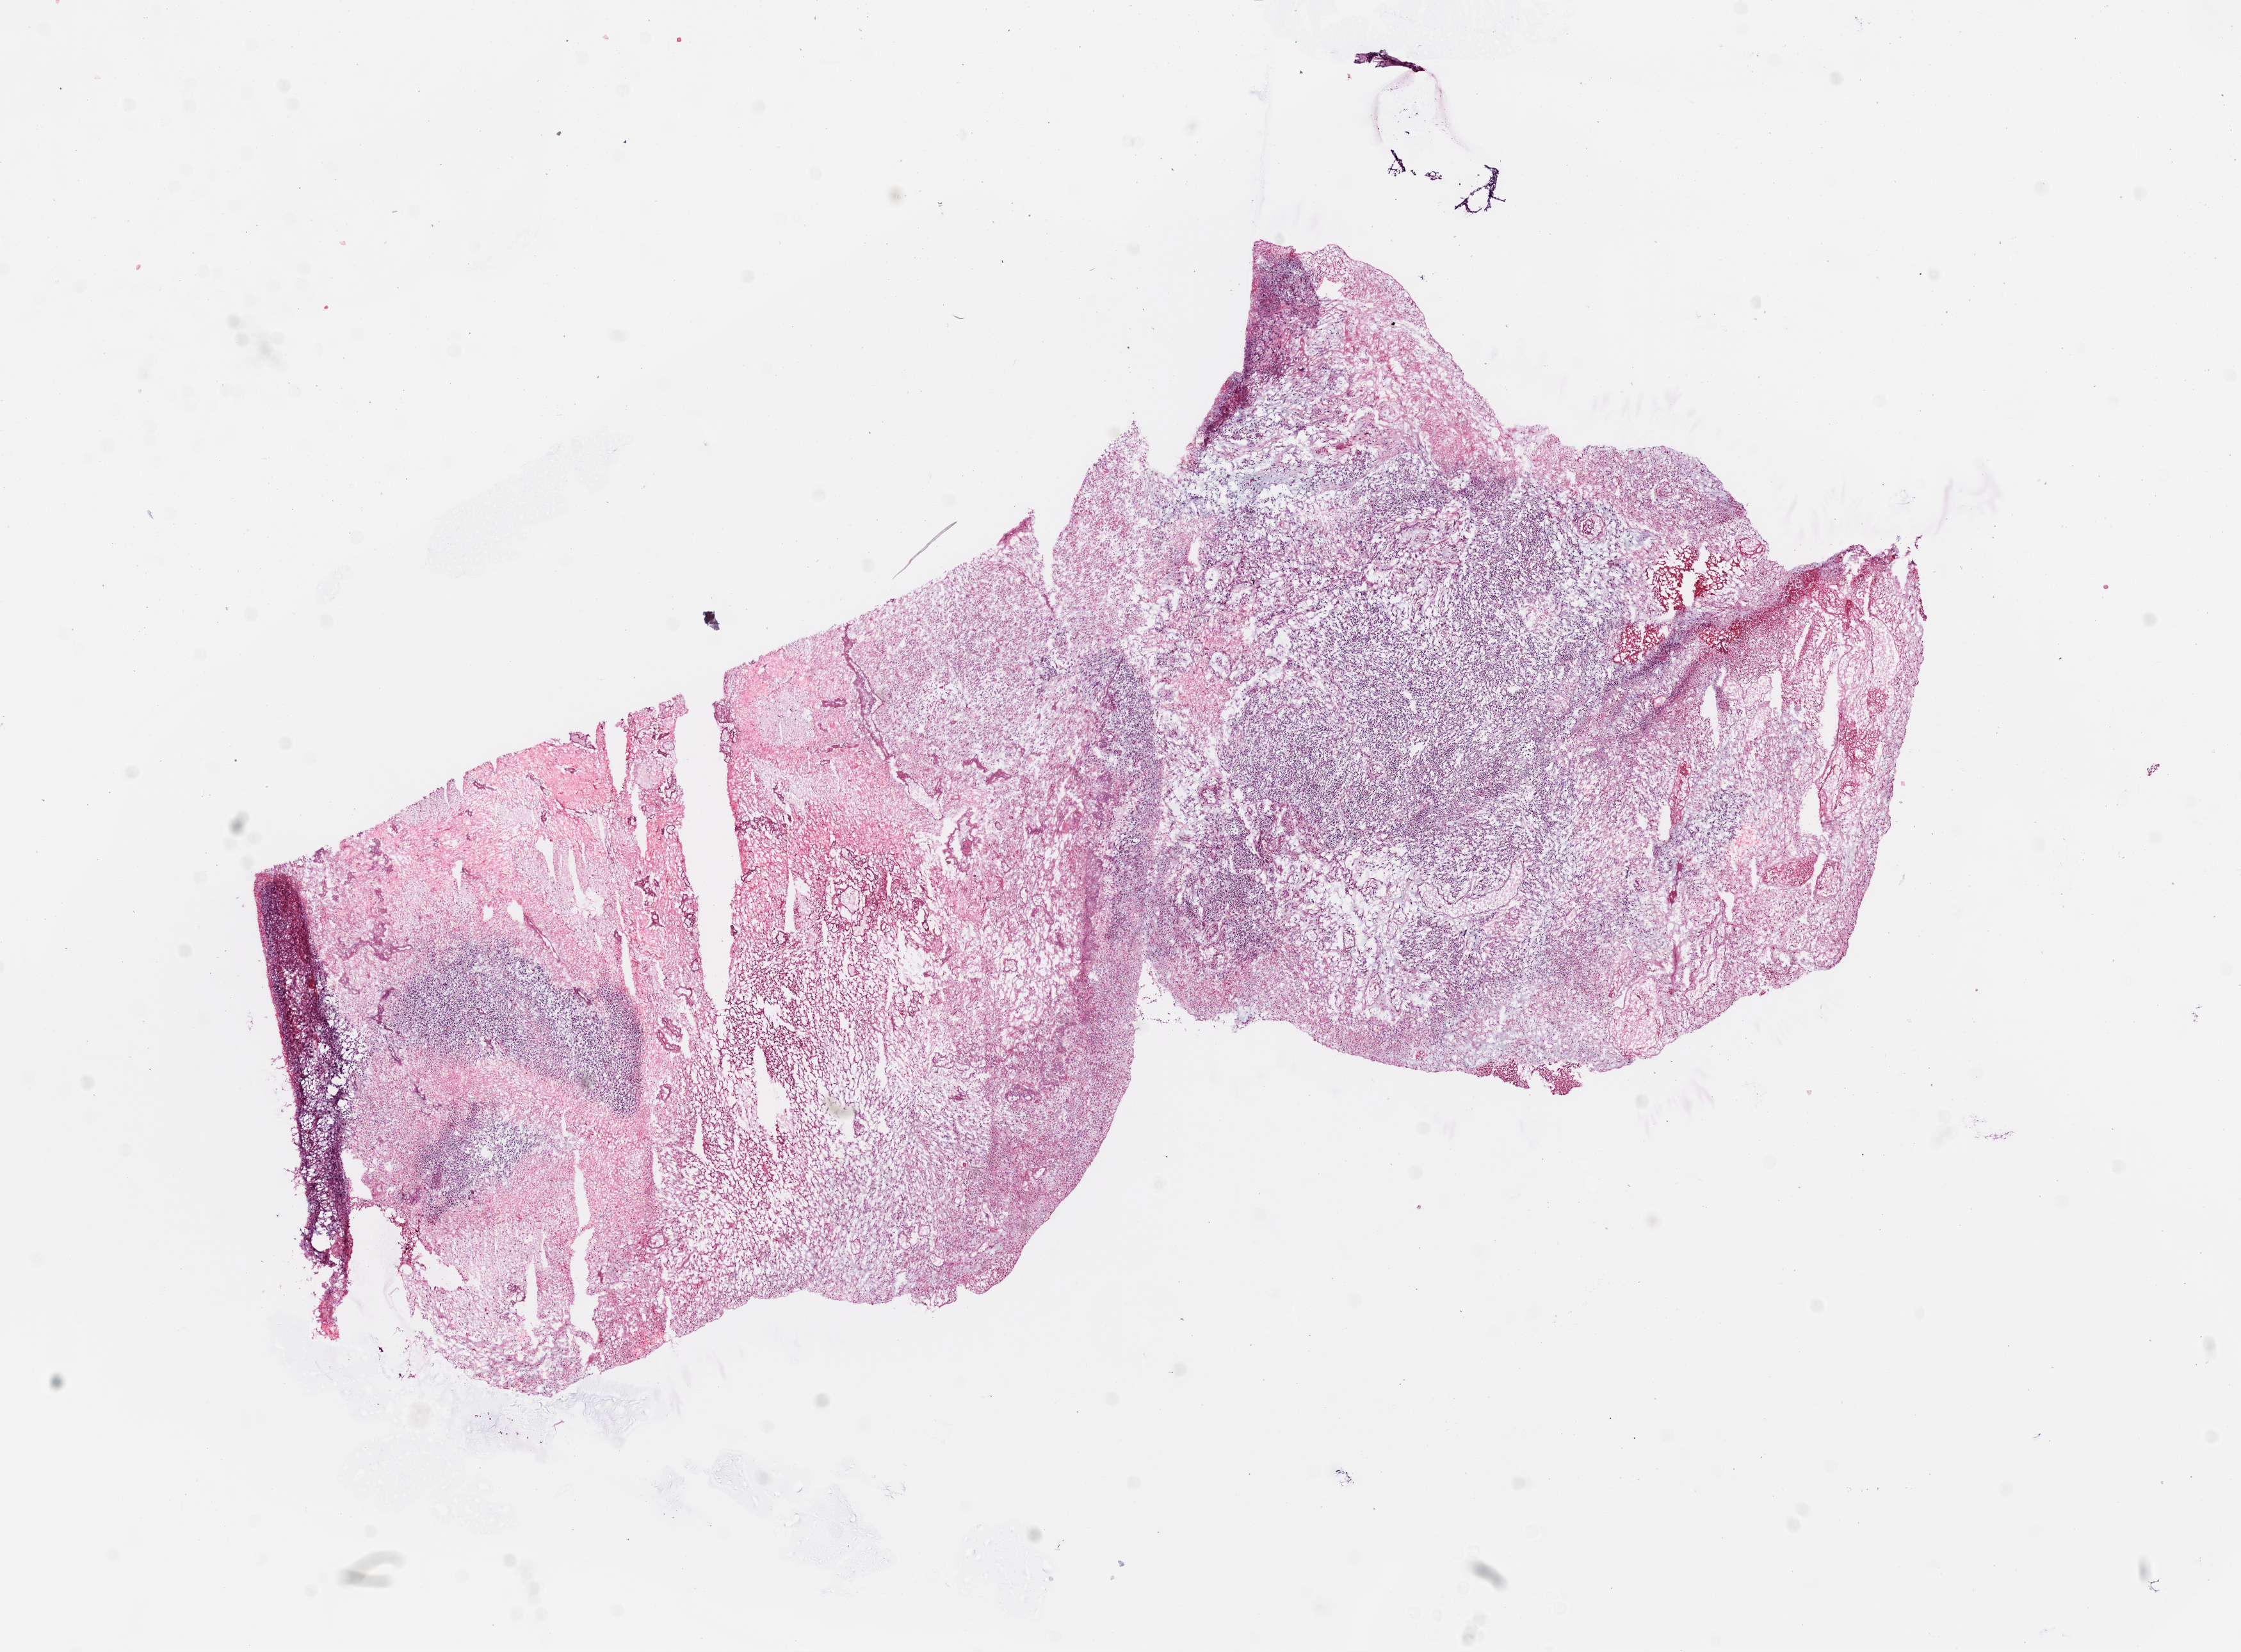
Digitized H&E tissue section (whole slide) — shown as a low-resolution overview of the whole scanned area (about 14.0 x 10.4 mm, slide scanned at 20x); frozen section from the bottom of the tissue portion; brain, primary tumour sample. Patient: female, age at initial diagnosis 47 years.
Diagnosis: Glioblastoma.